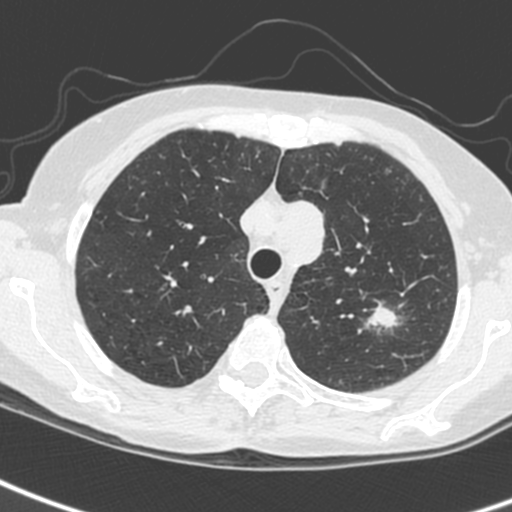
Low-dose screening chest CT, one axial slice. Slice 197 of 242 in the series (ordered by position). 120 kVp. Lung window (W 1500 / L -600 HU). 512 × 512 image matrix, field of view 284 × 284 mm.
Structures marked on this image (outlined manually by an expert reader):
- lesion 1 (tumor, upper lobe of left lung): bounding box <372,307,398,327> (left, top, right, bottom; pixels)
- lesion 3 (tumor, upper lobe of left lung): <294,200,325,264>